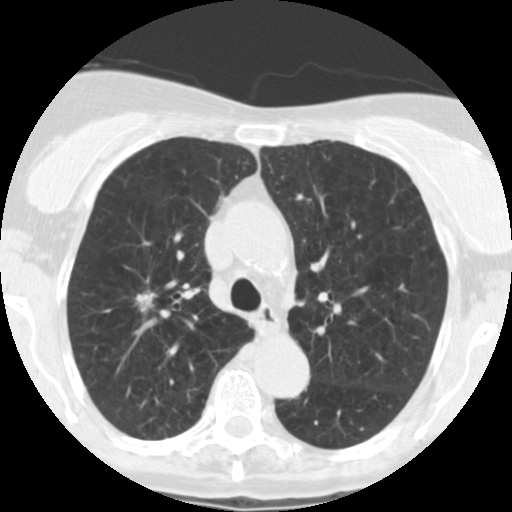
Chest CT (low-dose screening protocol), one axial image; baseline screening round; lung window (W 1500 / L -600 HU); 2.5 mm slice thickness; standard (soft-tissue) reconstruction kernel (STANDARD). Female participant, aged 67 years at enrolment.
Expert-annotated lung lesion, box from (x=114, y=280) to (x=171, y=324) px. The screening reader recorded 6 non-calcified nodules or masses ≥4 mm on this exam (right upper lobe, right middle lobe, left lower lobe, right middle lobe, left lower lobe, left lower lobe); which of them this box marks is not recorded. Participant outcome: lung cancer diagnosed 15 days after this screen — adenocarcinoma, NOS, right upper lobe, moderately differentiated (G2), stage IA (AJCC 6th edition), 14 mm at pathology.